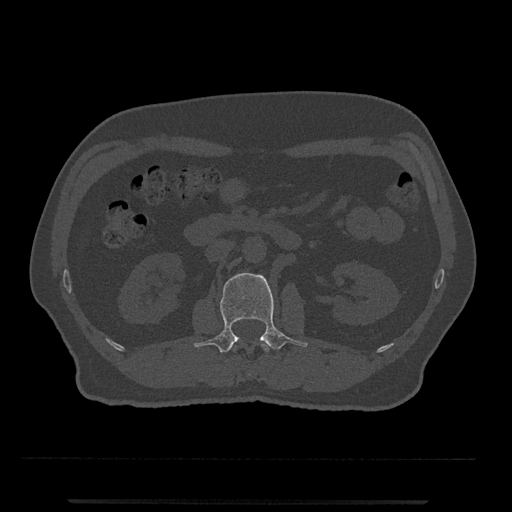
CT including the spine, one axial slice; slice 279 of 797 in the series (ordered by position); bone window (W 1800 / L 400 HU); 0.5 mm slice thickness; 512 × 512 image matrix, field of view 419 × 419 mm. Patient: male, 63 years. Case-level facts recorded for this patient, not image findings: primary cancer: prostate.
Outlined on this slice (semi-automatic segmentation, software-assisted and operator-edited):
- L1 vertebra: box from (x=233, y=343) to (x=269, y=352) px
- L2 vertebra: (x=194, y=273)–(x=308, y=353)